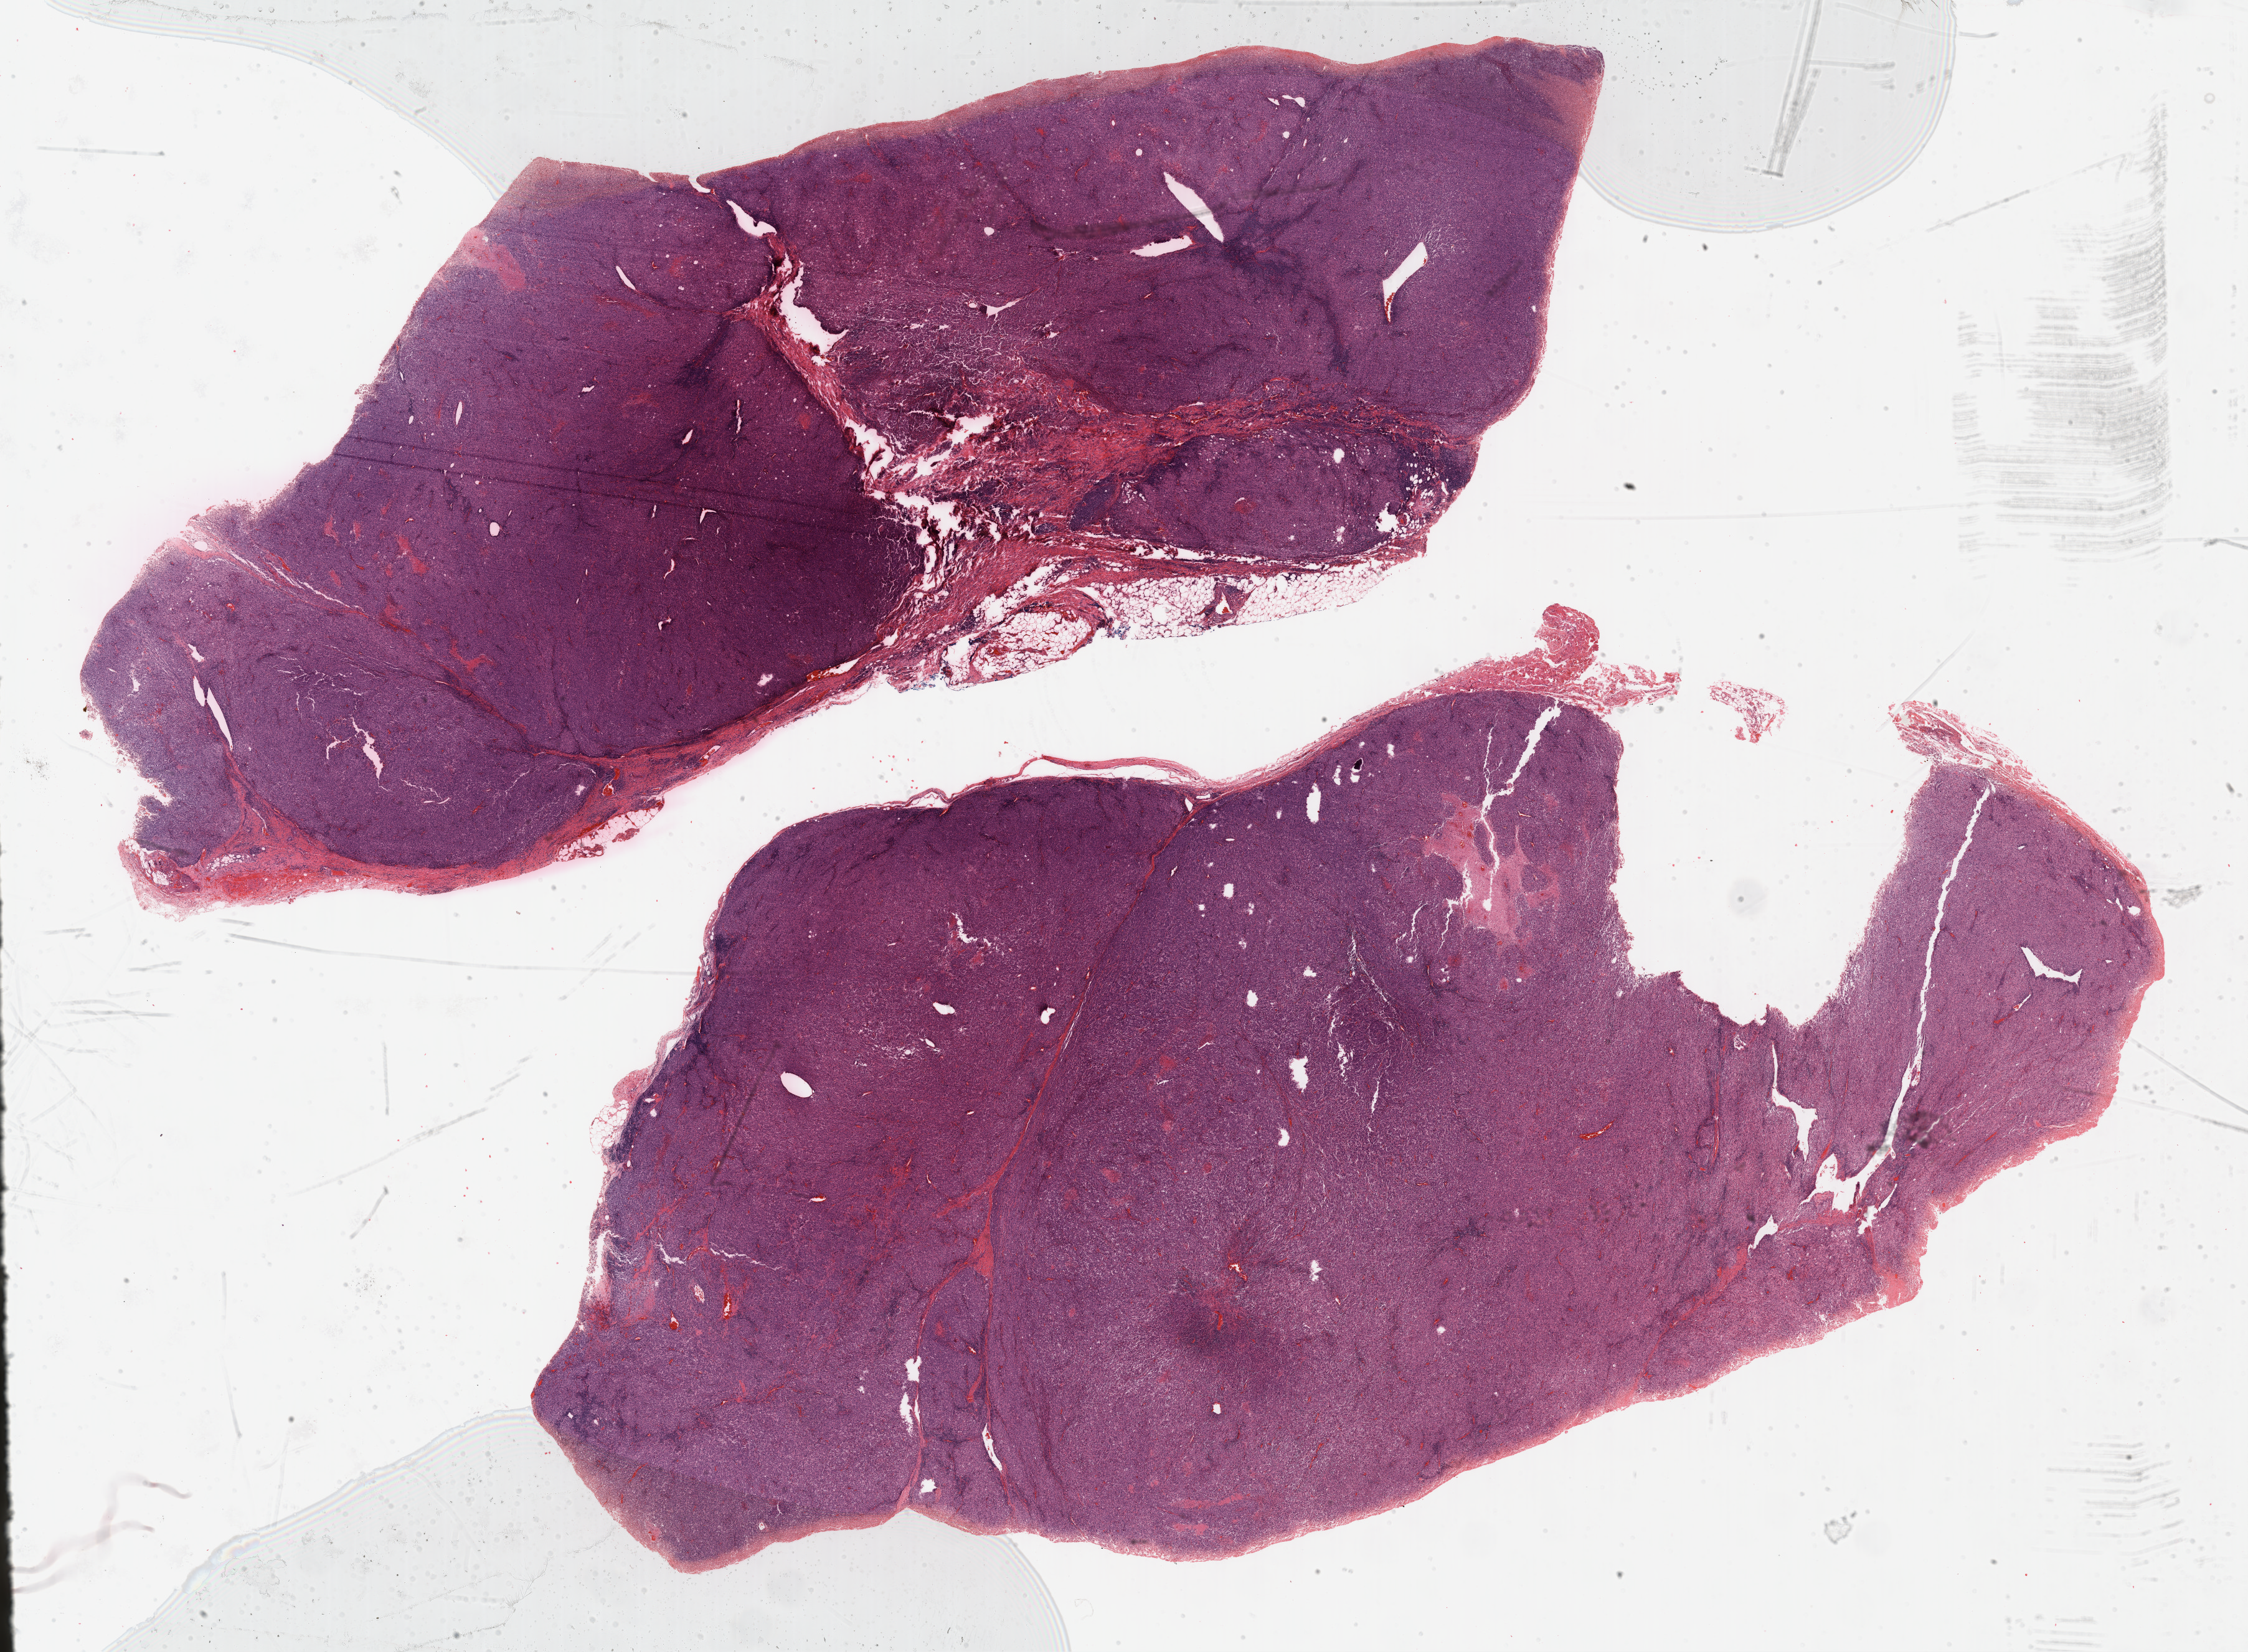
Digitized H&E-stained tissue section (whole slide), shown as a low-resolution overview of the whole scanned area (about 29.2 x 21.5 mm, from a 40x scan). Formalin-fixed paraffin-embedded (FFPE) diagnostic section. Metastatic tumour sample, sampled site not recorded. Male patient; age at initial diagnosis 63 years.
This section: metastatic tumour tissue. Patient diagnosis: Malignant melanoma, NOS.